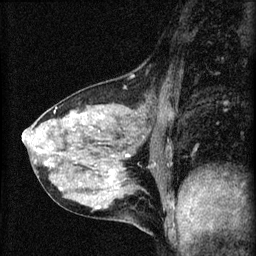
Breast MRI (dynamic contrast-enhanced), one sagittal slice; position 22 of 60 along the scan axis; dynamic contrast-enhanced series, image 2 of 4 at this slice position (ordered by acquisition); 1.5 T; TE 4.2 ms, TR 8.2 ms; 2 mm slice thickness; 256 × 256 image matrix. Female patient, age 41 years.
Structures marked on this image (semi-automatically segmented with operator editing):
- analysis volume of interest (the breast-tissue region the enhancement analysis was run in; not a lesion): bounding box <23,91,166,210> (left, top, right, bottom; pixels)
- tumour enhancement mask (voxels above the 70 % enhancement threshold inside the analysis volume of interest): <23,133,130,209>